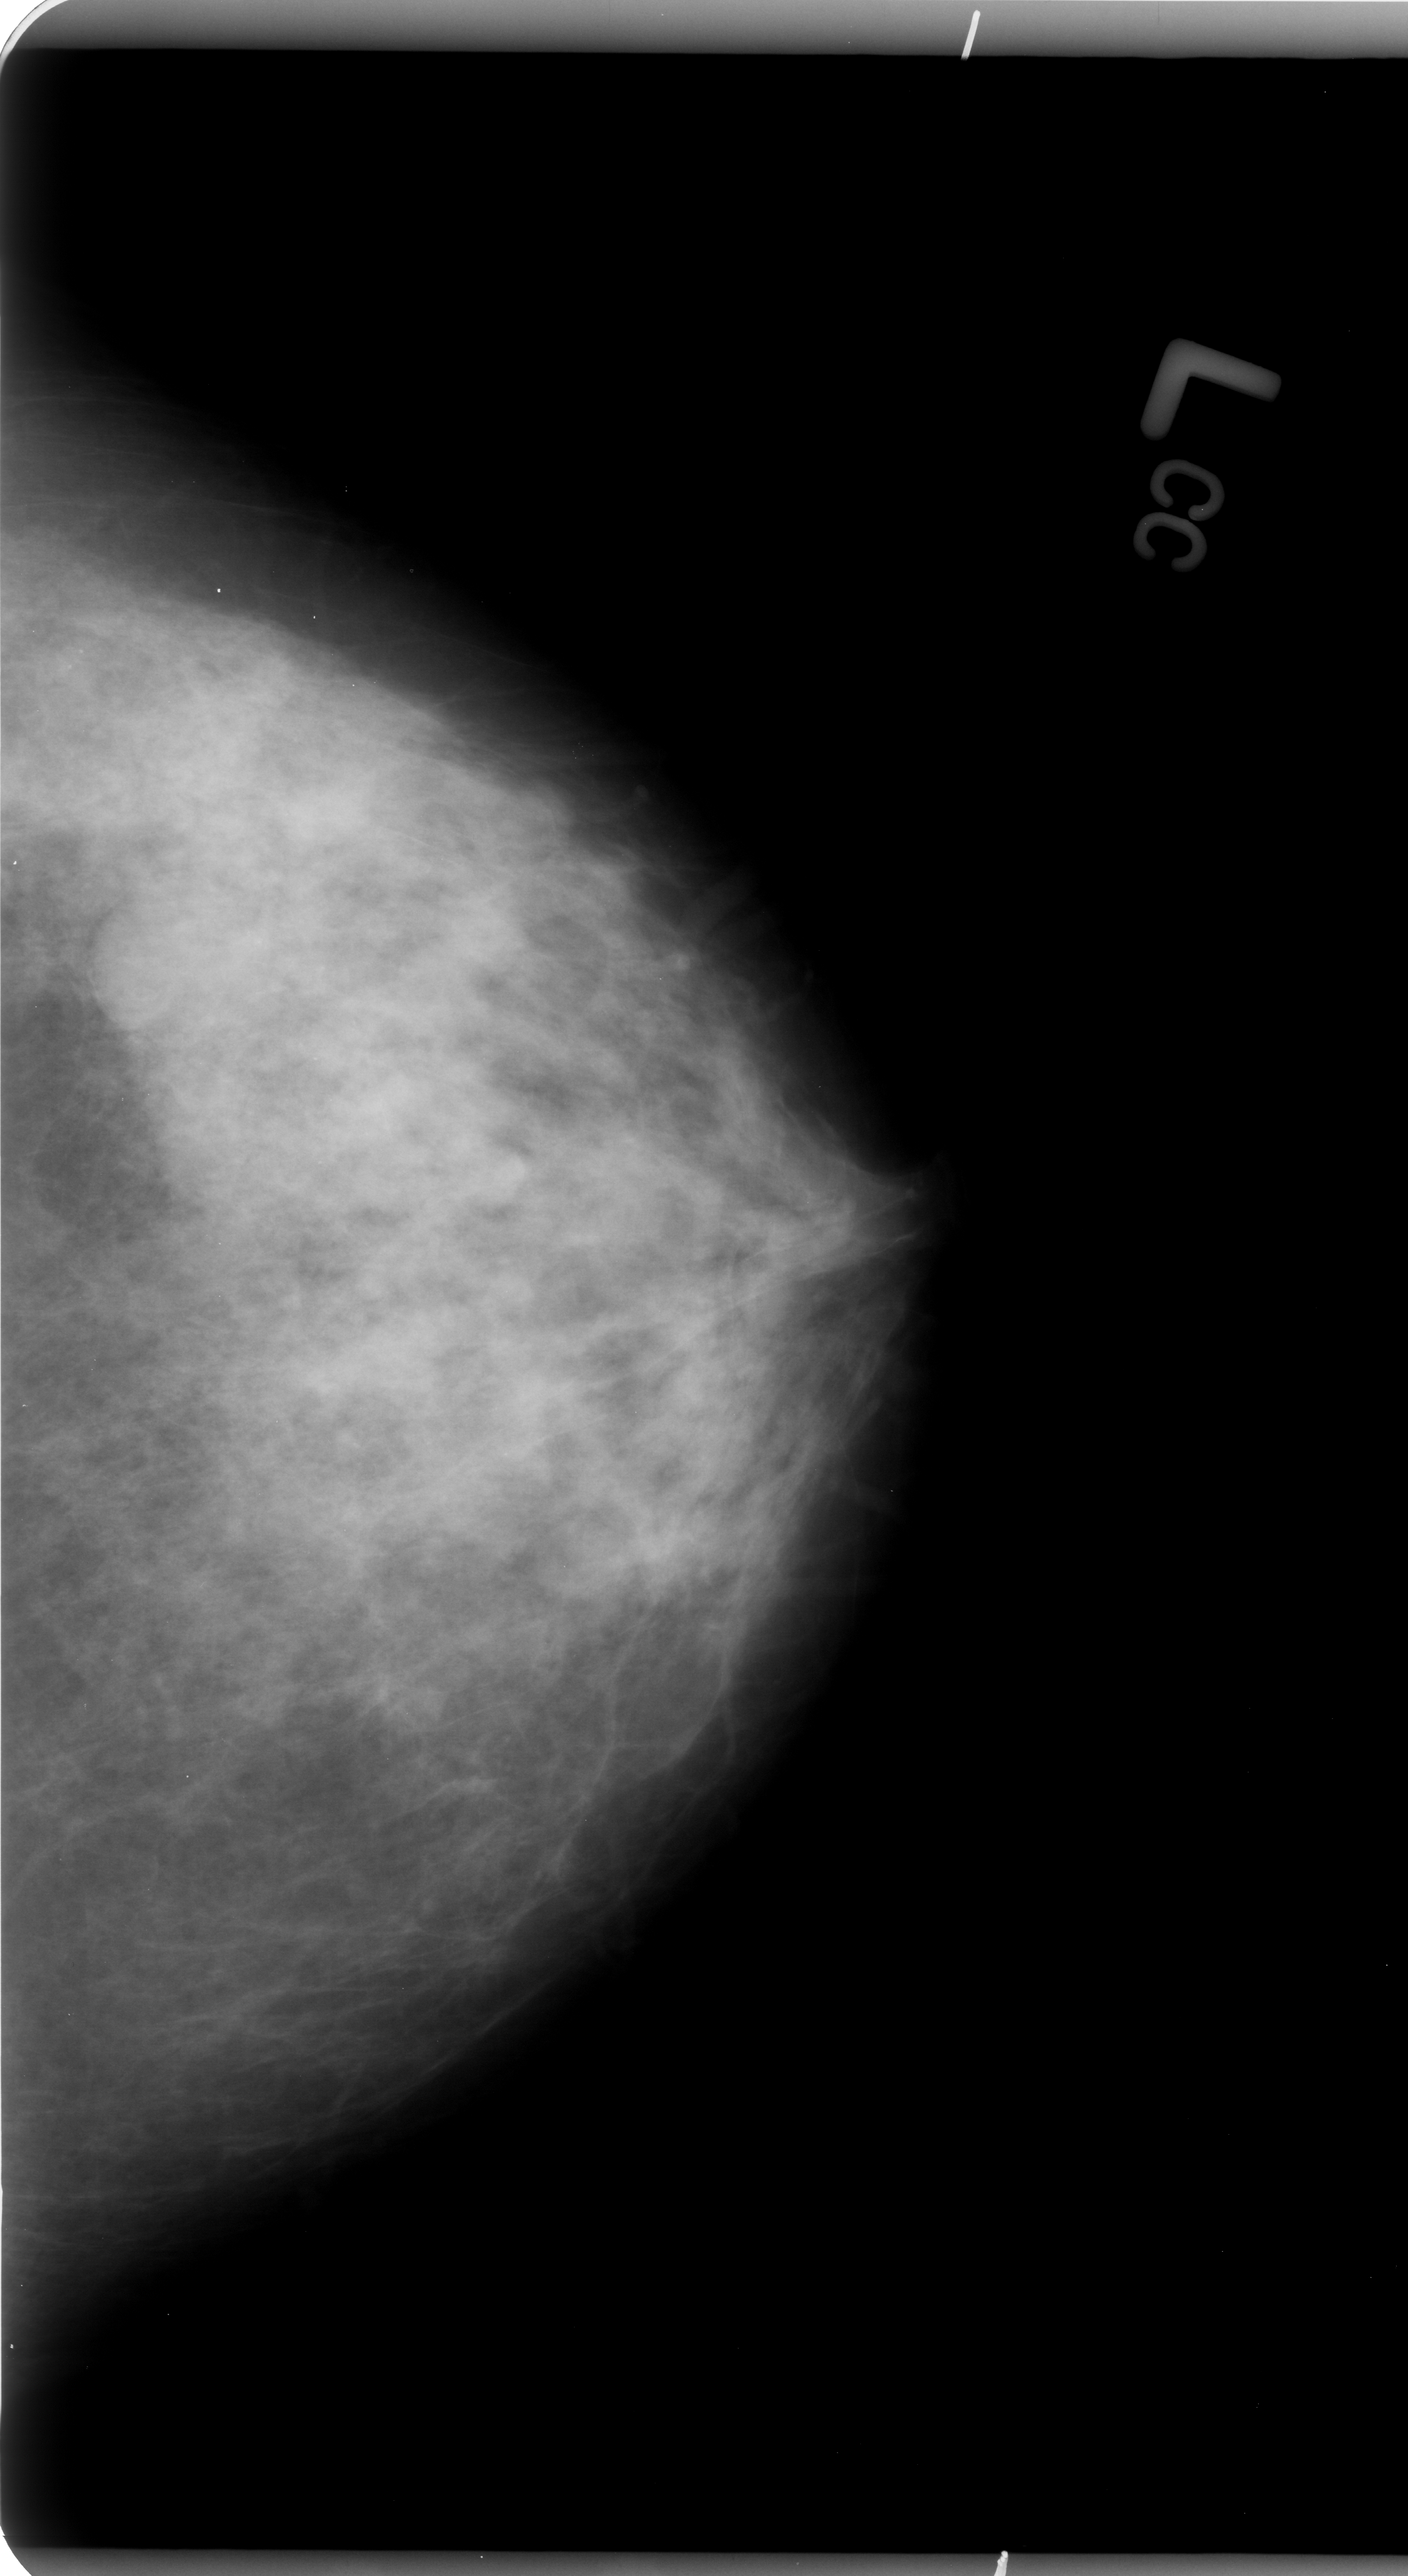
Scanned film-screen mammogram. Left breast. CC view. Breast composition: heterogeneously dense (BI-RADS density category 3 of 4). 1408 × 2576 image matrix.
Expert-marked regions of interest on this film, with their recorded descriptors:
- mass, shape oval, margins circumscribed; BI-RADS assessment category 3; pathology (as recorded): benign: bounding box <77,918,185,1047> (left, top, right, bottom; pixels)